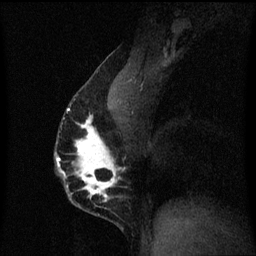
Breast MRI (dynamic contrast-enhanced), one sagittal slice; dynamic contrast-enhanced series, image 2 of 3 at this slice position (ordered by acquisition); 1.5 T; TE 4.2 ms, TR 8.4 ms; 2 mm slice thickness; 256 × 256 image matrix, field of view 200 × 200 mm. Patient: female, 40 years.
Structures marked on this image (semi-automatically segmented with operator editing):
- analysis volume of interest (the breast-tissue region the enhancement analysis was run in; not a lesion): bounding box (x1, y1, x2, y2) in pixels: (56, 84, 124, 211)
- tumour enhancement mask (voxels above the 70 % enhancement threshold inside the analysis volume of interest): (57, 110, 121, 203)